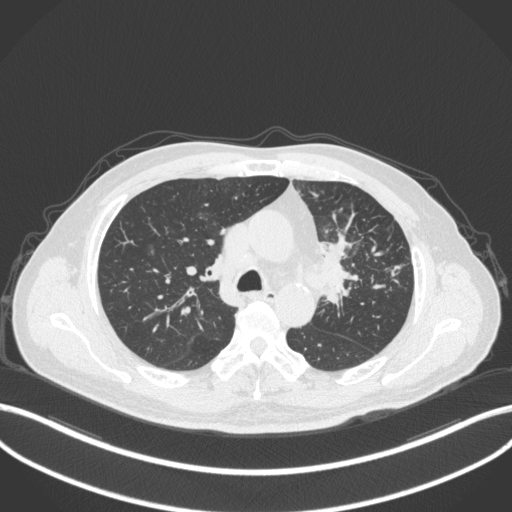
Chest CT, one axial slice. Position 234 of 386 along the scan axis. Reconstruction kernel B31f. 120 kVp. Lung window (W 1500 / L -600 HU). 1 mm slice thickness. 512 × 512 image matrix, field of view 400 × 400 mm. Patient: male, 69 years. From the clinical record (not read from this slice): clinical TNM (as recorded): T2a N2 M0; histopathological grade: G2-3.
Outlined on this slice (rectangle marked by the reading radiologist):
- lung tumour (recorded histology: adenocarcinoma): bounding box (x1, y1, x2, y2) in pixels: (314, 231, 355, 311)